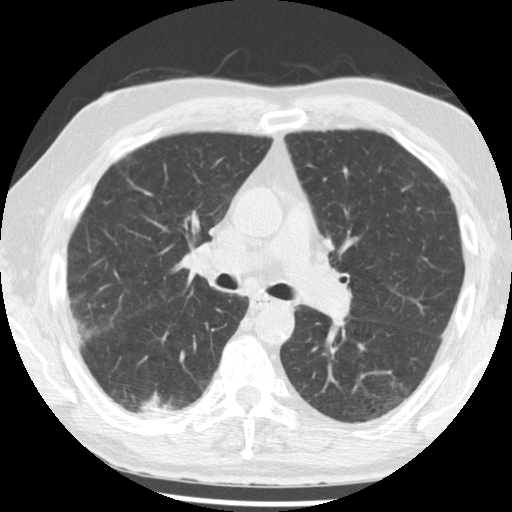
Low-dose screening chest CT, one axial slice; slice 124 of 221 in the series (ordered by position); 120 kVp; lung window (W 1500 / L -600 HU); 2.5 mm slice thickness; 512 × 512 image matrix, field of view 350 × 350 mm.
Annotated regions visible in this slice (expert manual segmentation):
- lesion 1 (tumor, lower lobe of right lung): bounding box <137,393,179,417> (left, top, right, bottom; pixels)